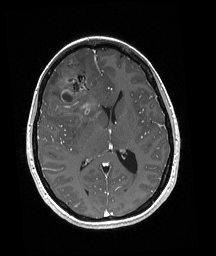
Brain MRI from a brain-tumour surgery series, one axial slice; slice 92 of 192 in the series (ordered by position); T1-weighted post-contrast; 1 mm slice thickness; 216 × 256 image matrix, field of view 211 × 250 mm. Case-level facts recorded for this patient, not image findings: histopathology: Oligodendroglioma; WHO grade: 3; IDH mutation: yes; tumour location: Right Frontal.
Structures marked on this image (manually delineated by an expert):
- tumour: bounding box [x1, y1, x2, y2] px = [50, 61, 99, 120]